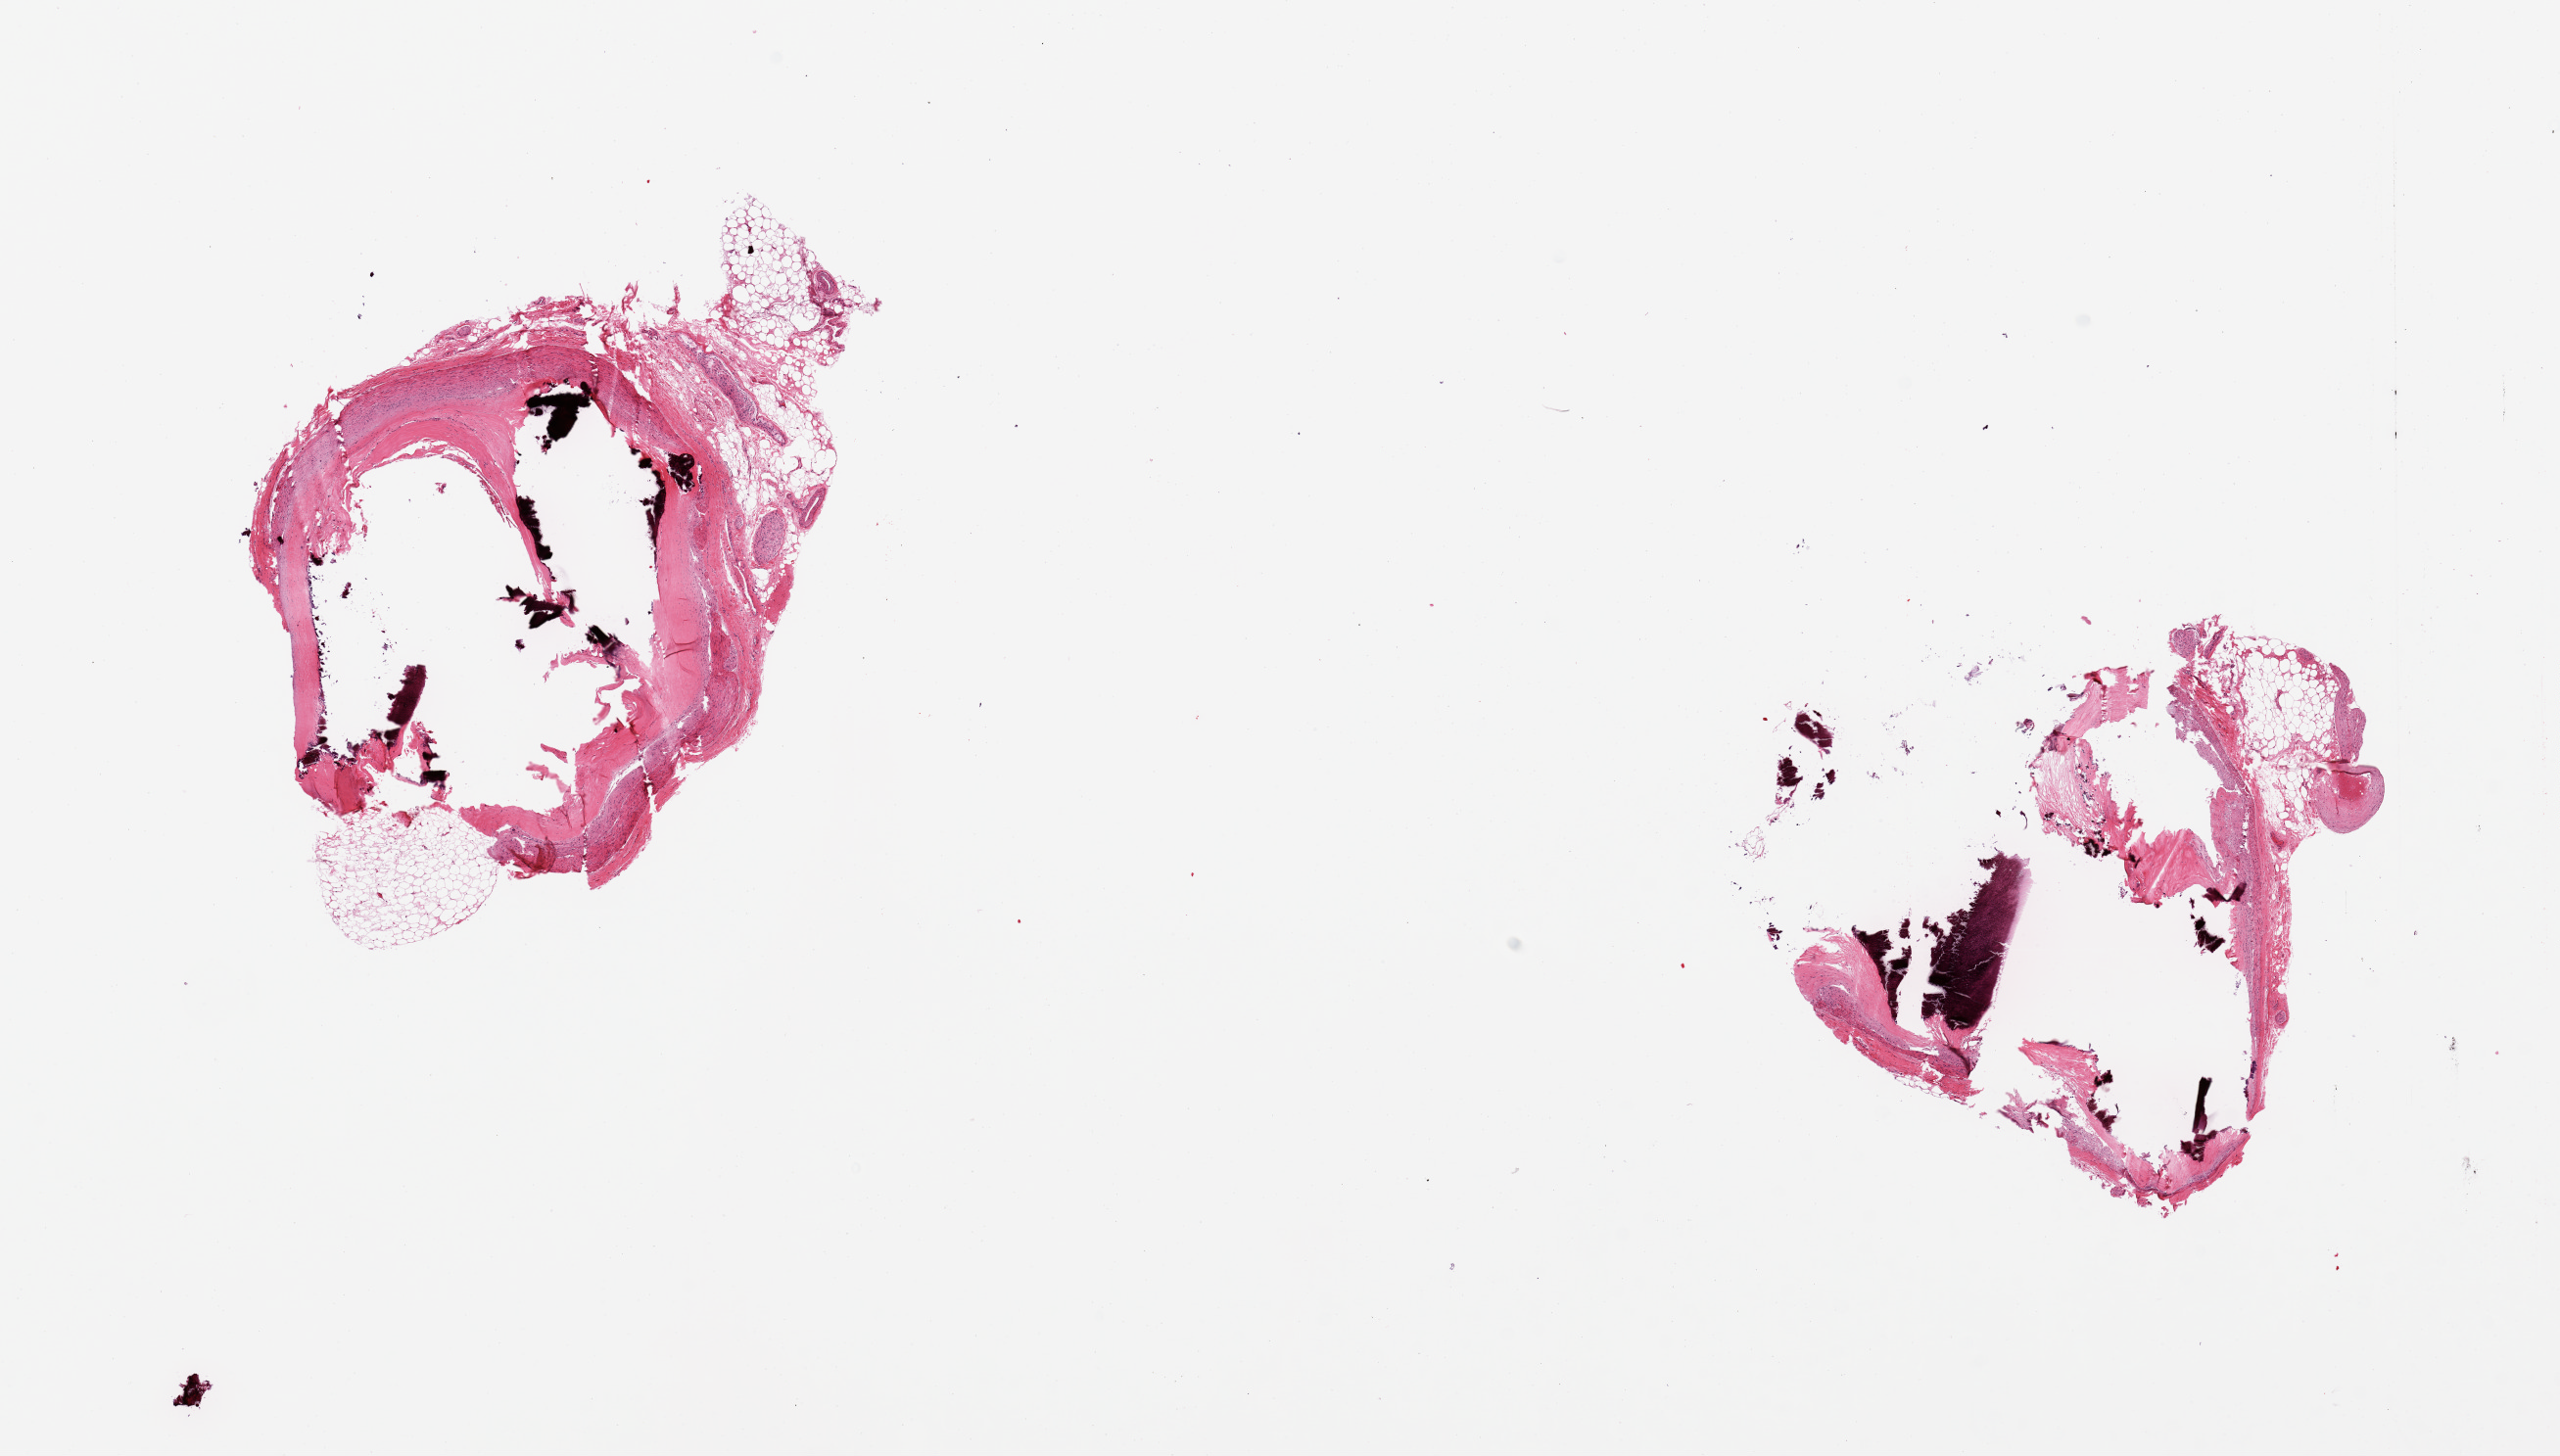
Digitized hematoxylin and eosin (H&E)-stained section, brightfield — shown as a low-resolution overview of the whole scanned area (about 20.7 x 11.8 mm, slide scanned at 20x); PAXgene-fixed, paraffin-embedded tissue; section of coronary artery (target tissue); donor tissue sample.
- review note (as recorded): 2 pieces, one of them fragmenetd; marked atherosclerotic changes with calcifications significantly compromising lumen, attachment of adipose tissue and nerve